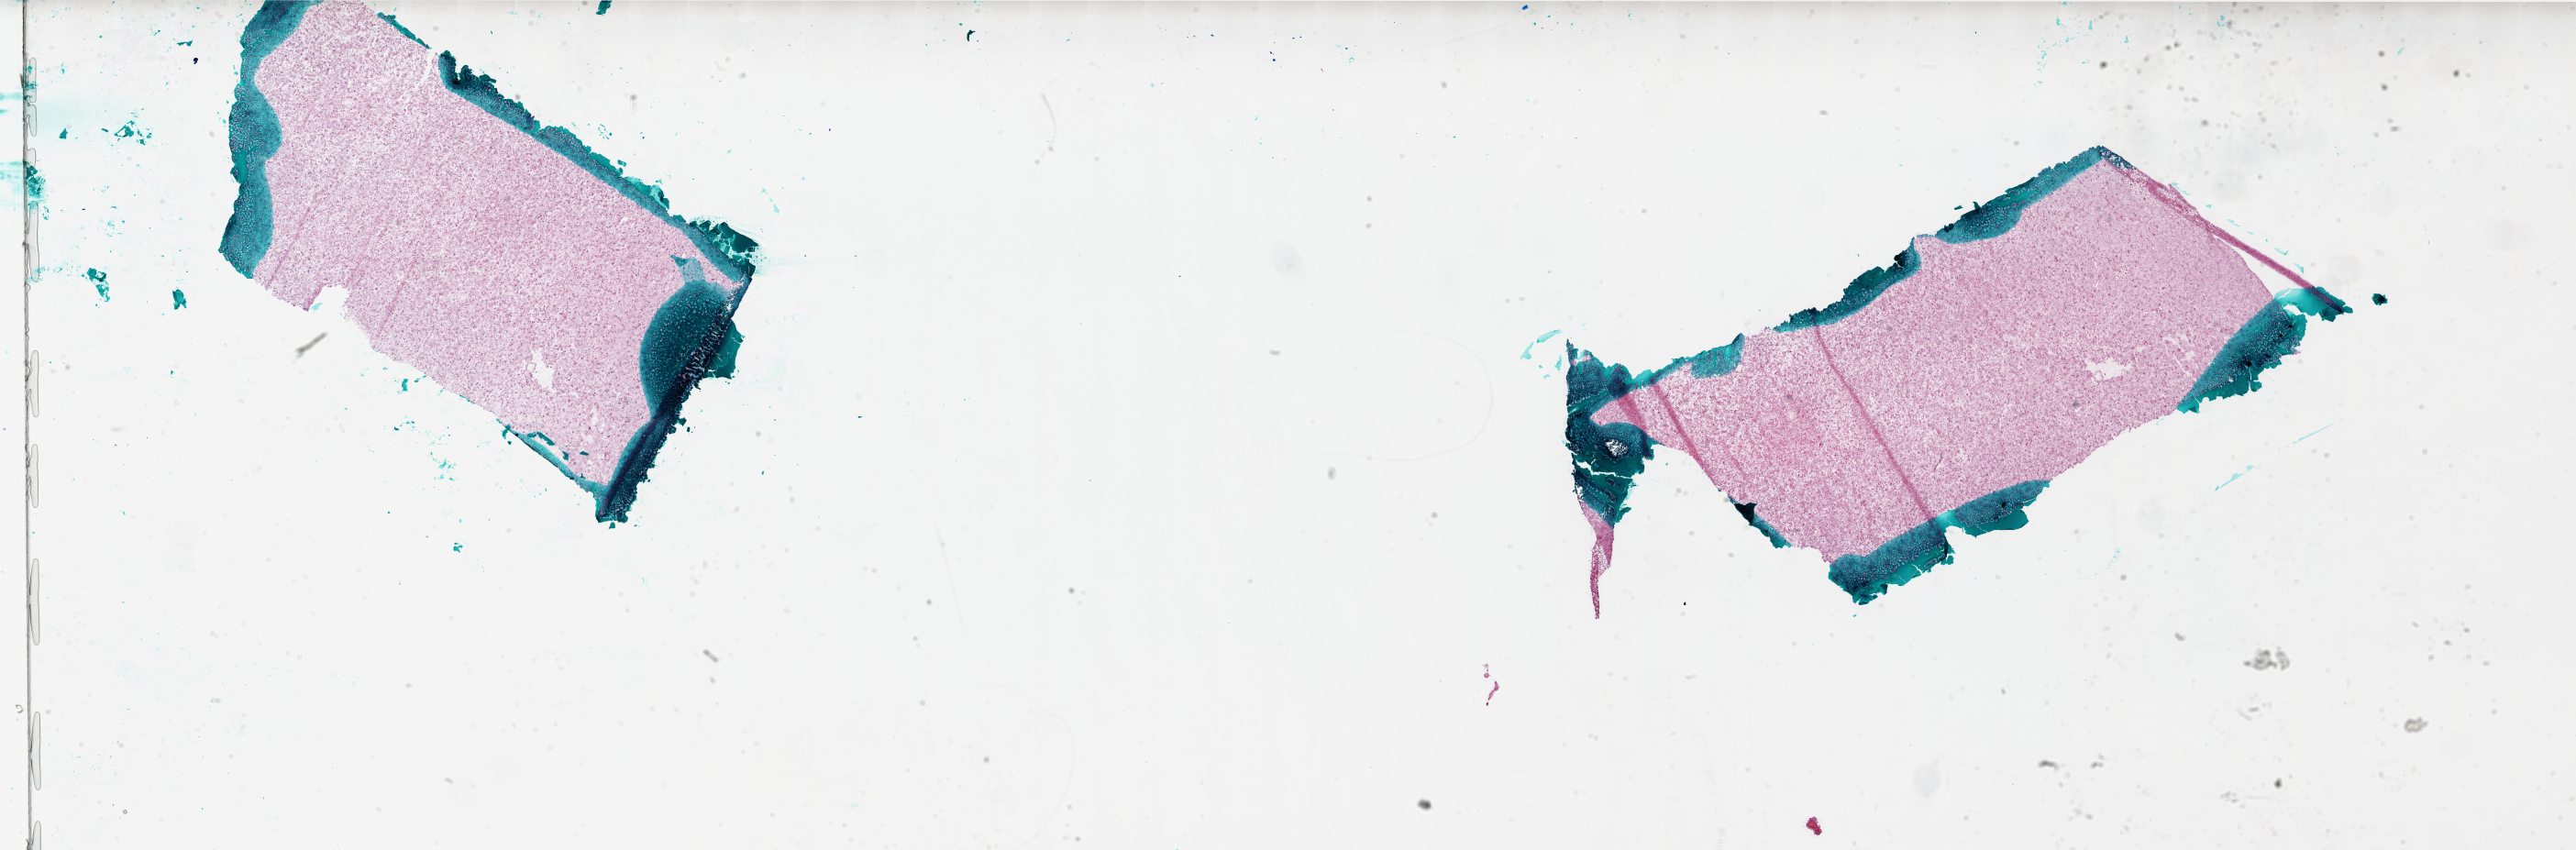
H&E whole-slide image — whole scanned area (about 45.0 x 14.8 mm, from a 20x scan) shown as a low-resolution overview, frozen section from the bottom of the tissue portion, primary tumour sample from the brain. Patient: female, age at initial diagnosis 44 years. Slide review estimates, as recorded: tumour cells 100%, tumour nuclei 100%, normal cells 0%, stromal cells 0%, necrosis 0%.
- diagnosis: Glioblastoma